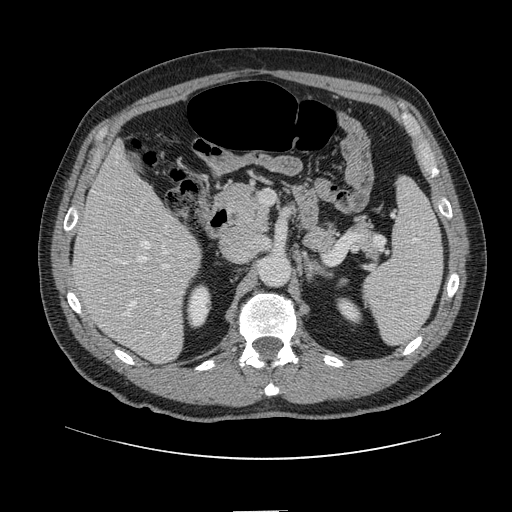
Contrast-enhanced abdominal CT, one axial slice; slice 65 of 161 in the series (ordered by position); 120 kVp; soft-tissue window (W 400 / L 40 HU); 2.5 mm slice thickness; 512 × 512 image matrix, field of view 412 × 412 mm. Male patient, age 66 years. From the clinical record (not read from this slice): diagnosis: colorectal cancer liver metastases, imaged before liver resection; multiple liver metastases: no; largest metastasis: 3.5 cm; disease in both lobes: no.
Structures marked on this image (outlined manually by an expert reader):
- hepatic veins: bounding box [x1, y1, x2, y2] px = [117, 156, 168, 336]
- liver: [74, 146, 201, 363]
- planned liver remnant (the part of the liver to remain after resection): [74, 146, 177, 287]
- portal vein (with intrahepatic branches): [119, 212, 171, 315]